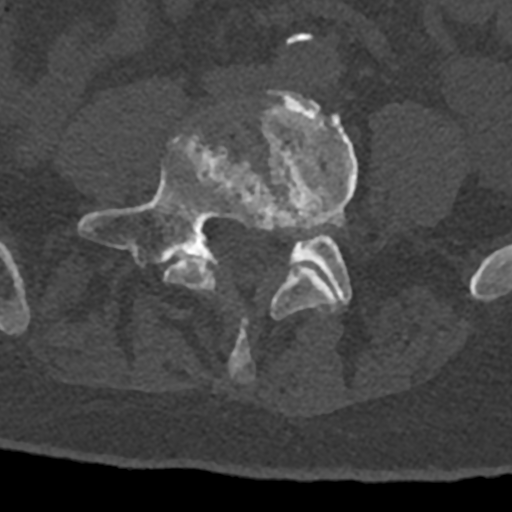
CT including the spine, one axial slice. Reconstruction kernel Br40s/3. 120 kVp. Bone window (W 1800 / L 400 HU). 512 × 512 image matrix, field of view 160 × 160 mm. Male patient, age 74 years. From the clinical record (not read from this slice): primary cancer: renal.
Structures marked on this image (semi-automatically segmented with operator editing):
- L4 vertebra: bounding box <163,90,358,383> (left, top, right, bottom; pixels)
- L5 vertebra: <78,130,352,305>